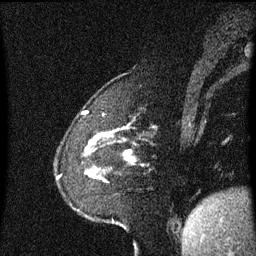
Breast MRI (dynamic contrast-enhanced), one sagittal slice. Slice 12 of 60 in the series (ordered by position). Dynamic contrast-enhanced series, image 2 of 3 at this slice position (ordered by acquisition). 1.5 T. TE 4.2 ms, TR 8.4 ms. 256 × 256 image matrix, field of view 200 × 200 mm. Patient: female, 60 years. From the clinical record (not read from this slice): setting: breast cancer imaged before/during neoadjuvant chemotherapy; receptor status: triple-negative.
Outlined on this slice (semi-automatically segmented with operator editing):
- analysis volume of interest (the breast-tissue region the enhancement analysis was run in; not a lesion): bounding box [x1, y1, x2, y2] px = [86, 142, 132, 183]
- tumour enhancement mask (voxels above the 70 % enhancement threshold inside the analysis volume of interest): [126, 152, 132, 159]